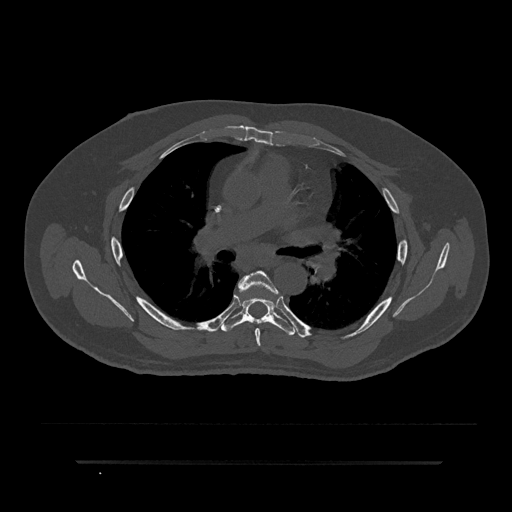
CT including the spine, one axial slice; position 547 of 797 along the scan axis; bone window (W 1800 / L 400 HU); 0.5 mm slice thickness; 512 × 512 image matrix, field of view 464 × 464 mm. Patient: male, 59 years. From the clinical record (not read from this slice): primary cancer: bile ducts; vertebrae with lytic lesions (as recorded): T10.
Outlined on this slice (semi-automatically segmented with operator editing):
- T5 vertebra: bounding box [x1, y1, x2, y2] px = [238, 271, 275, 346]
- T6 vertebra: [221, 283, 294, 336]